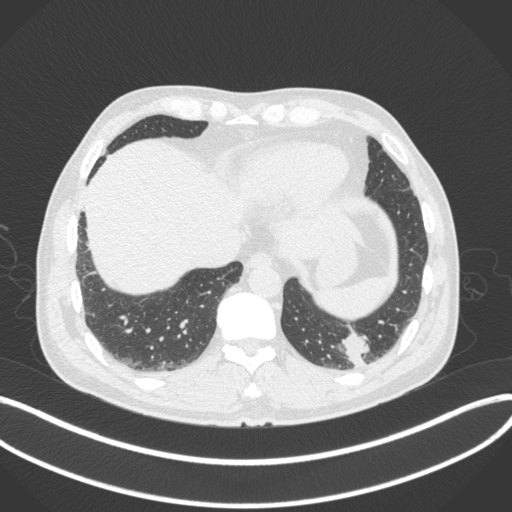
Chest CT, one axial slice. Position 58 of 313 along the scan axis. Reconstruction kernel B31f. 120 kVp. Lung window (W 1500 / L -600 HU). 1 mm slice thickness. 512 × 512 image matrix. Patient: male, 54 years. Case-level facts recorded for this patient, not image findings: clinical TNM (as recorded): T1c N0 M1; histopathological grade: G3.
Outlined on this slice (rectangle marked by the reading radiologist):
- lung tumour (recorded histology: adenocarcinoma): bounding box [x1, y1, x2, y2] px = [333, 328, 372, 365]